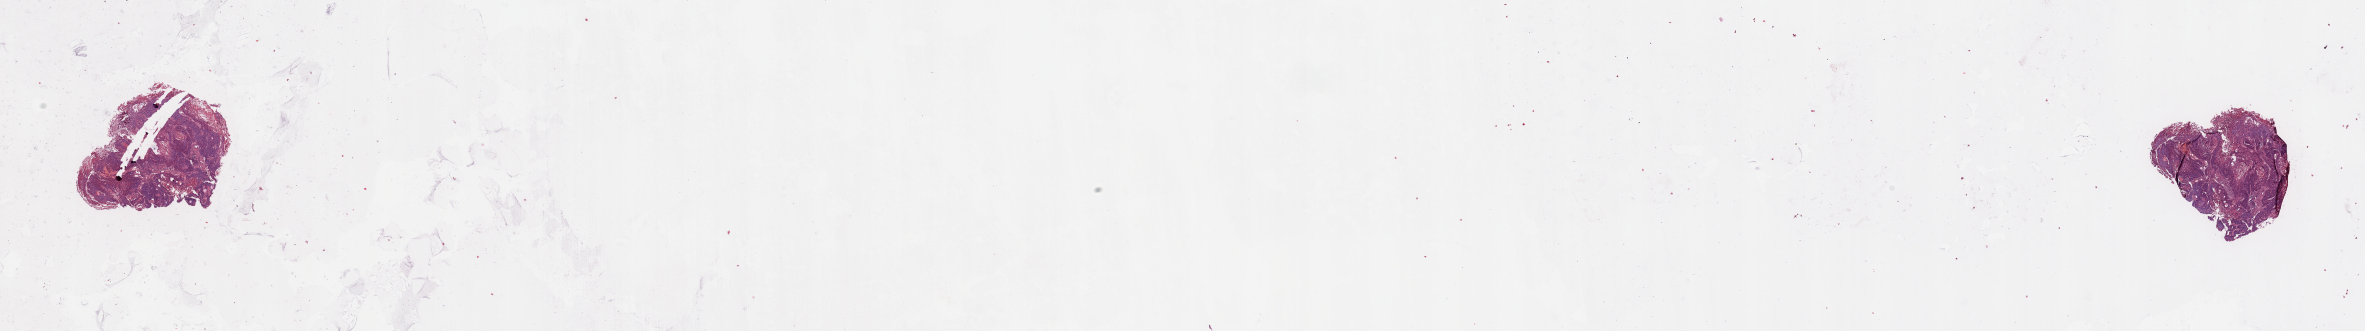
Hematoxylin and eosin (H&E) stained whole-slide image — low-resolution overview of the scanned area, about 37.4 x 5.2 mm, tumour tissue sample, sampled site: larynx. Patient: female, age 68 years. Histologic grade: G3 (poorly differentiated). Composition of this section per pathologist review: tumour nuclei 85%, necrosis 7%.
• diagnosis: Squamous cell carcinoma, NOS
• AJCC pathologic stage: IVA
• primary tumour site (as recorded): larynx